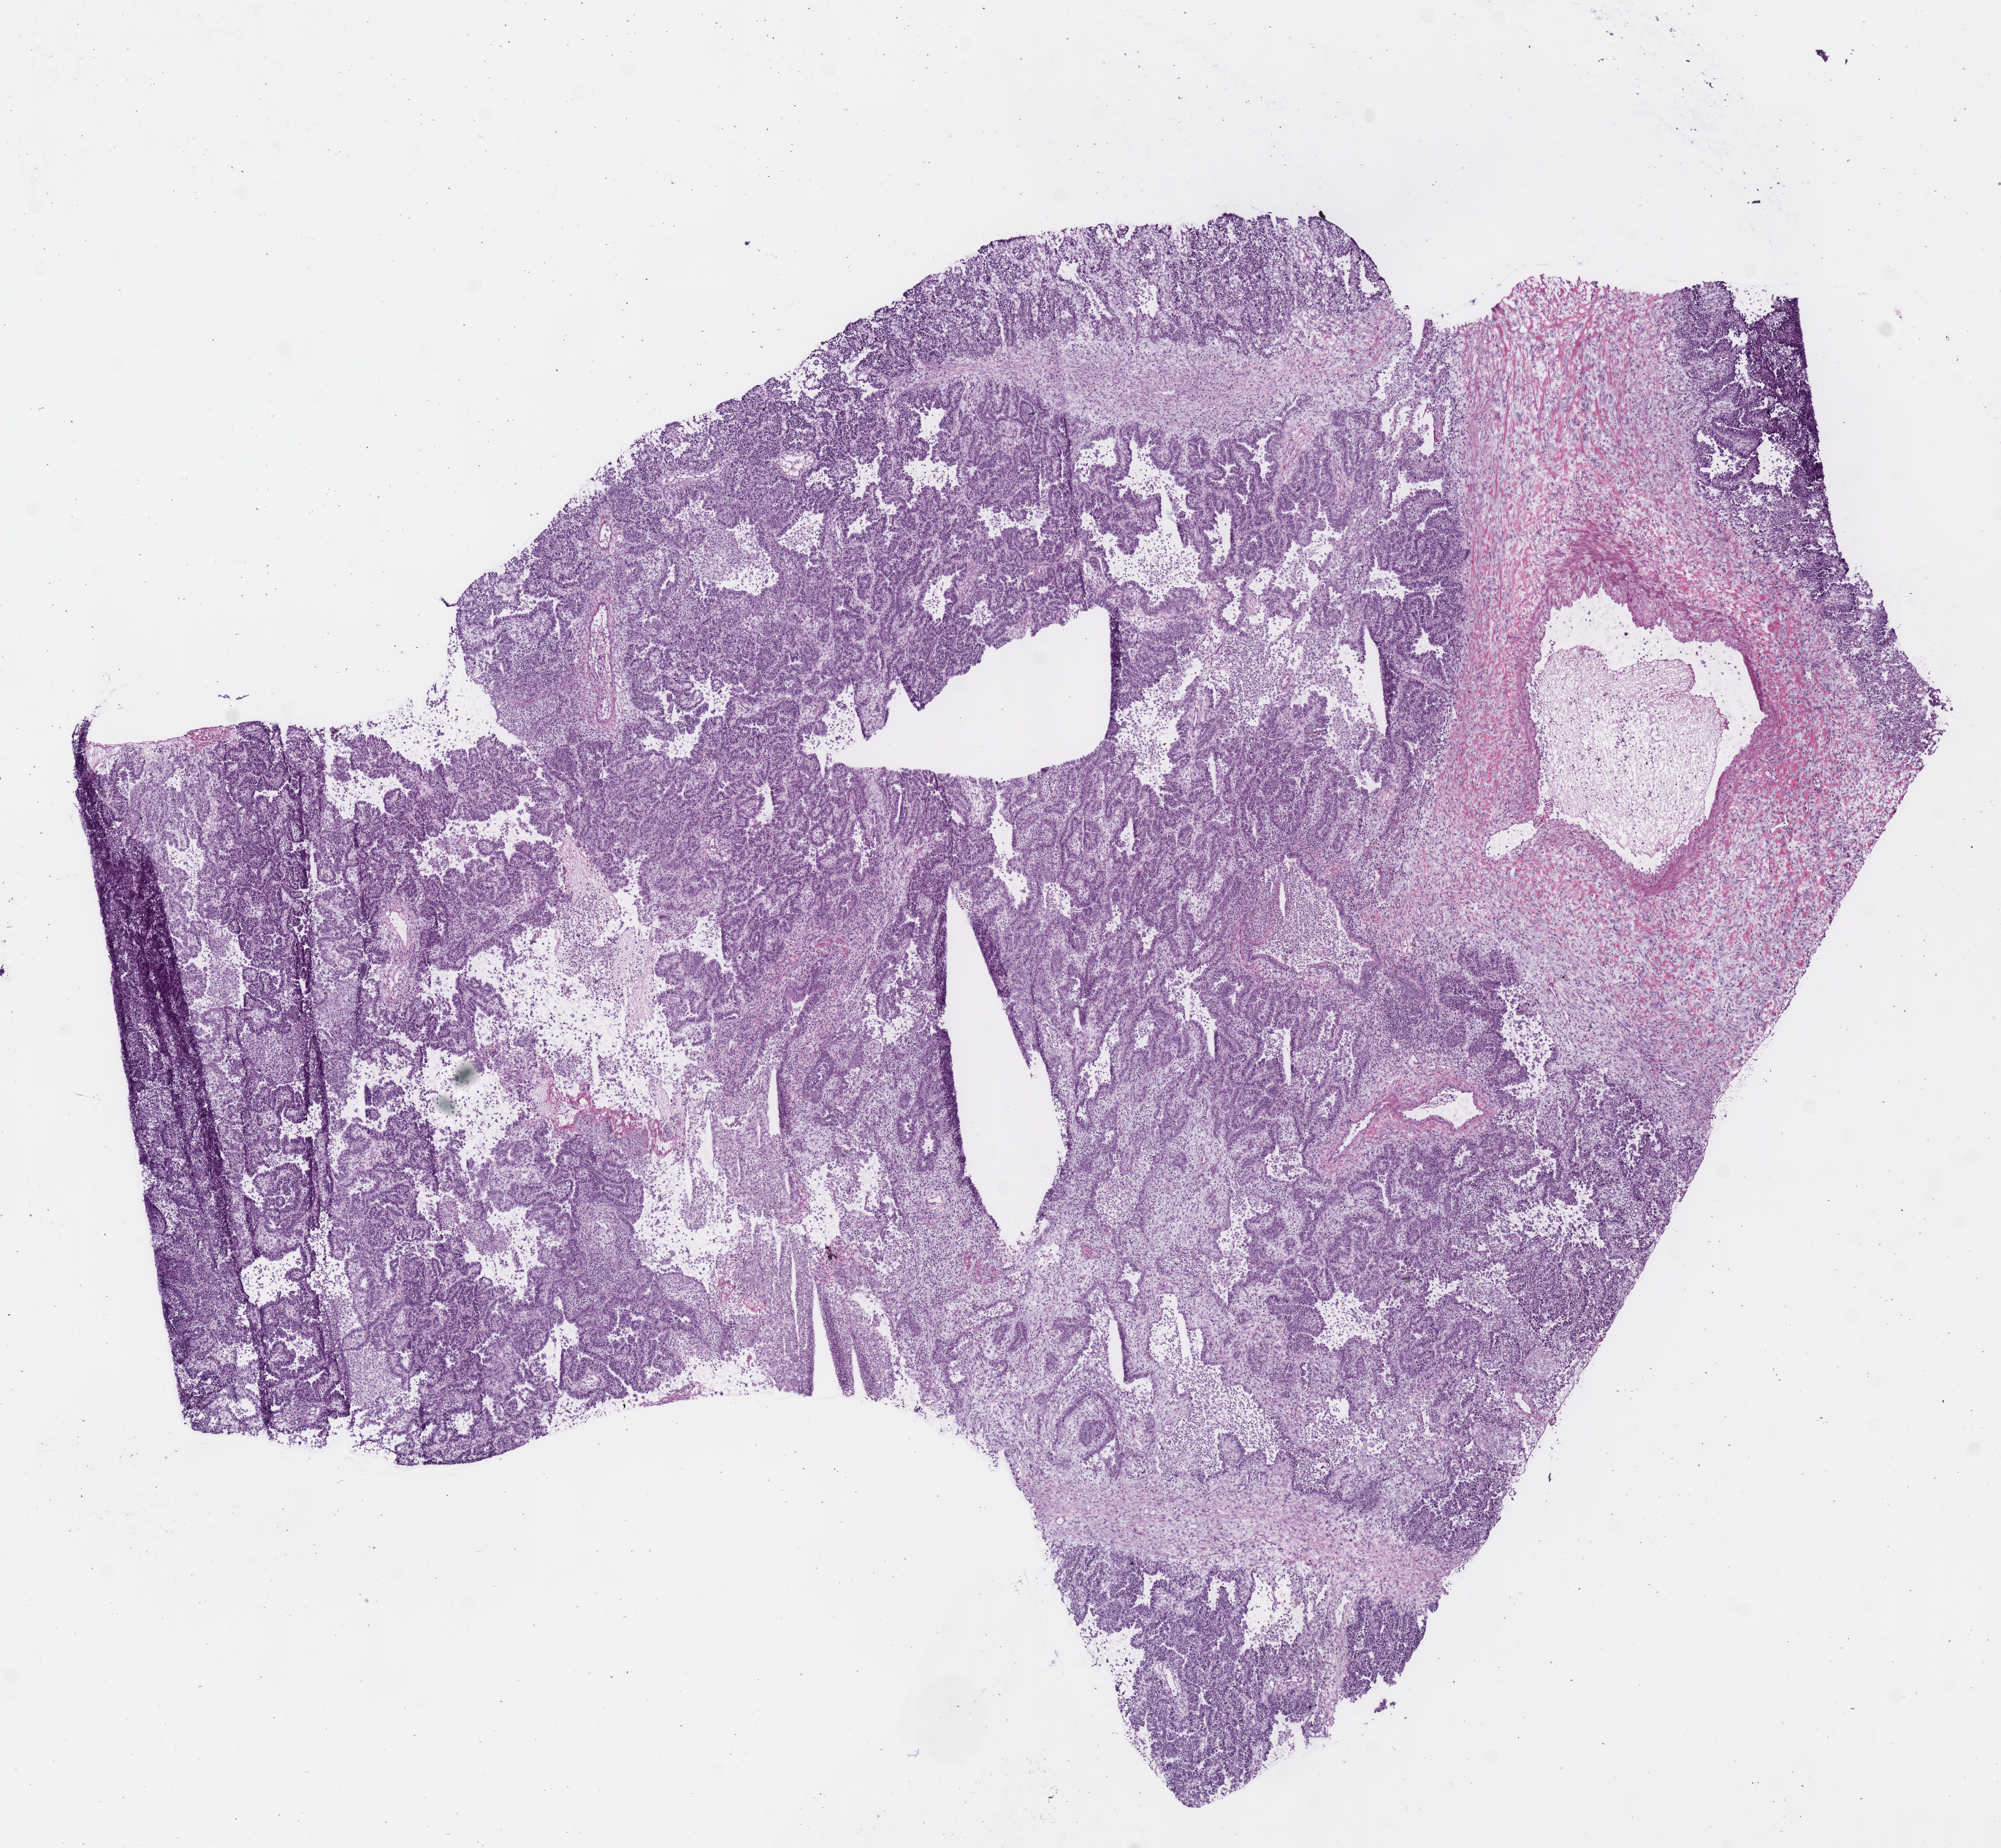
H&E-stained whole-slide image — whole scanned area (about 10.8 x 9.9 mm, from a 40x scan) shown as a low-resolution overview. Frozen section. Lung, primary tumour sample. Patient: female, age at initial diagnosis 69 years. Slide review estimates, as recorded: tumour cells 85%, tumour nuclei 70%, normal cells 0%, stromal cells 15%, necrosis 0%. Infiltration values recorded for this section: lymphocyte infiltration 20%, monocyte infiltration 0%, neutrophil infiltration 5%.
* histologic diagnosis: Adenocarcinoma with mixed subtypes (lower lobe, lung)
* AJCC pathologic stage: IIB
* laterality: right